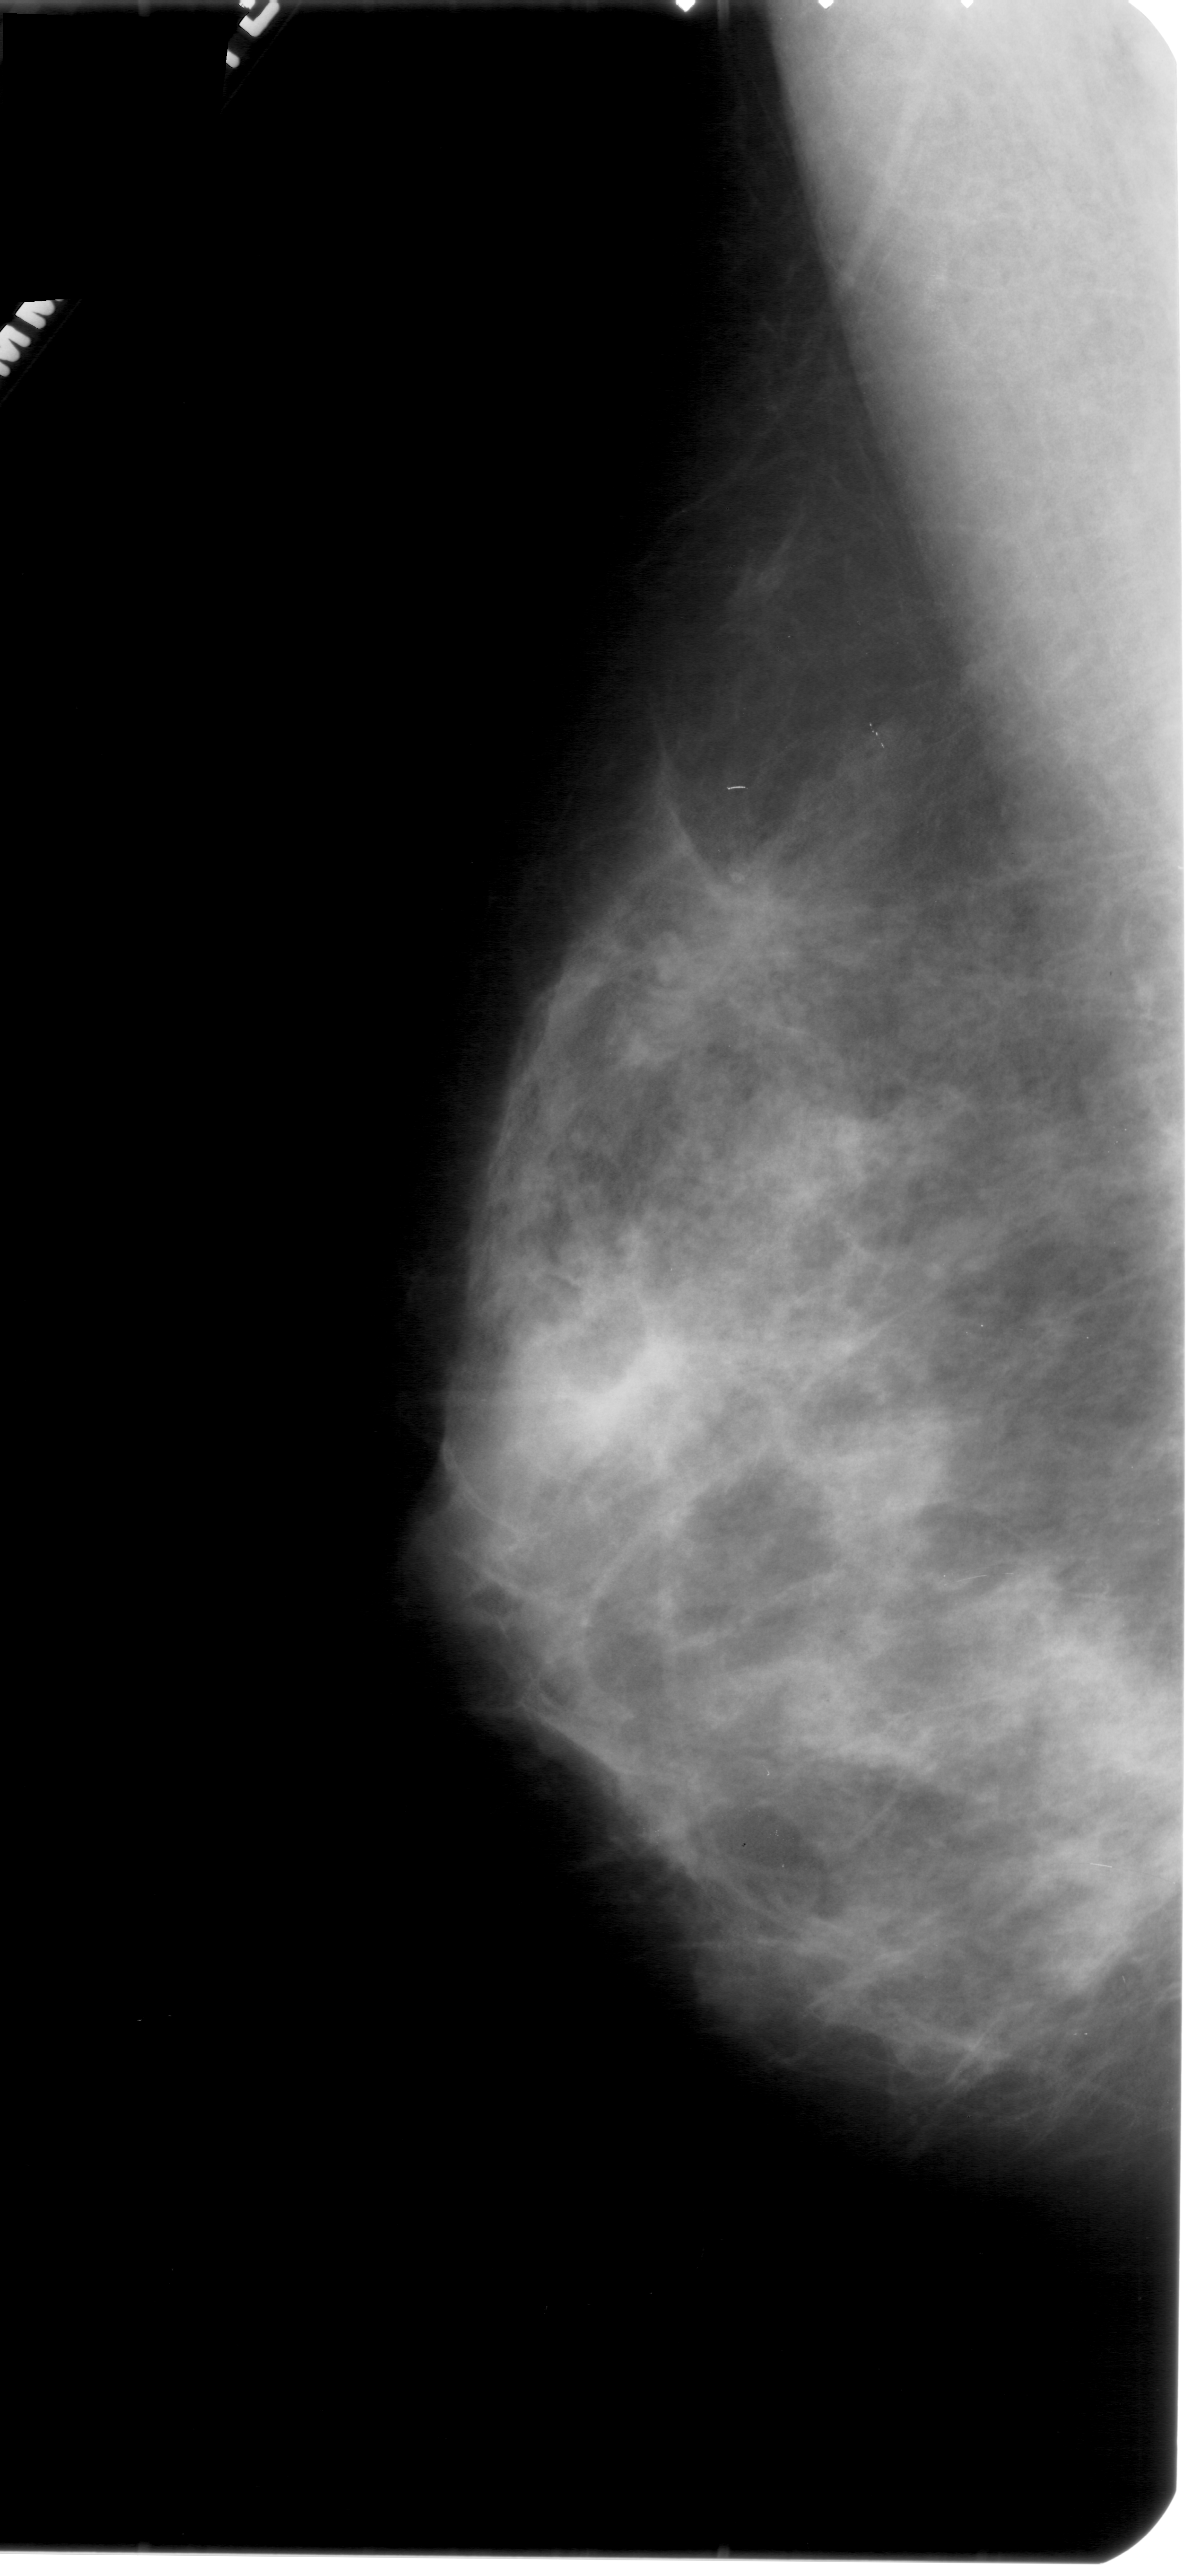
Digitized screen-film mammogram, left breast, mediolateral oblique (MLO) view, breast composition: extremely dense (BI-RADS density category 4 of 4).
- Abnormality record for this image: mass, shape irregular, margins spiculated; BI-RADS assessment category 4; pathology (as recorded): malignant.